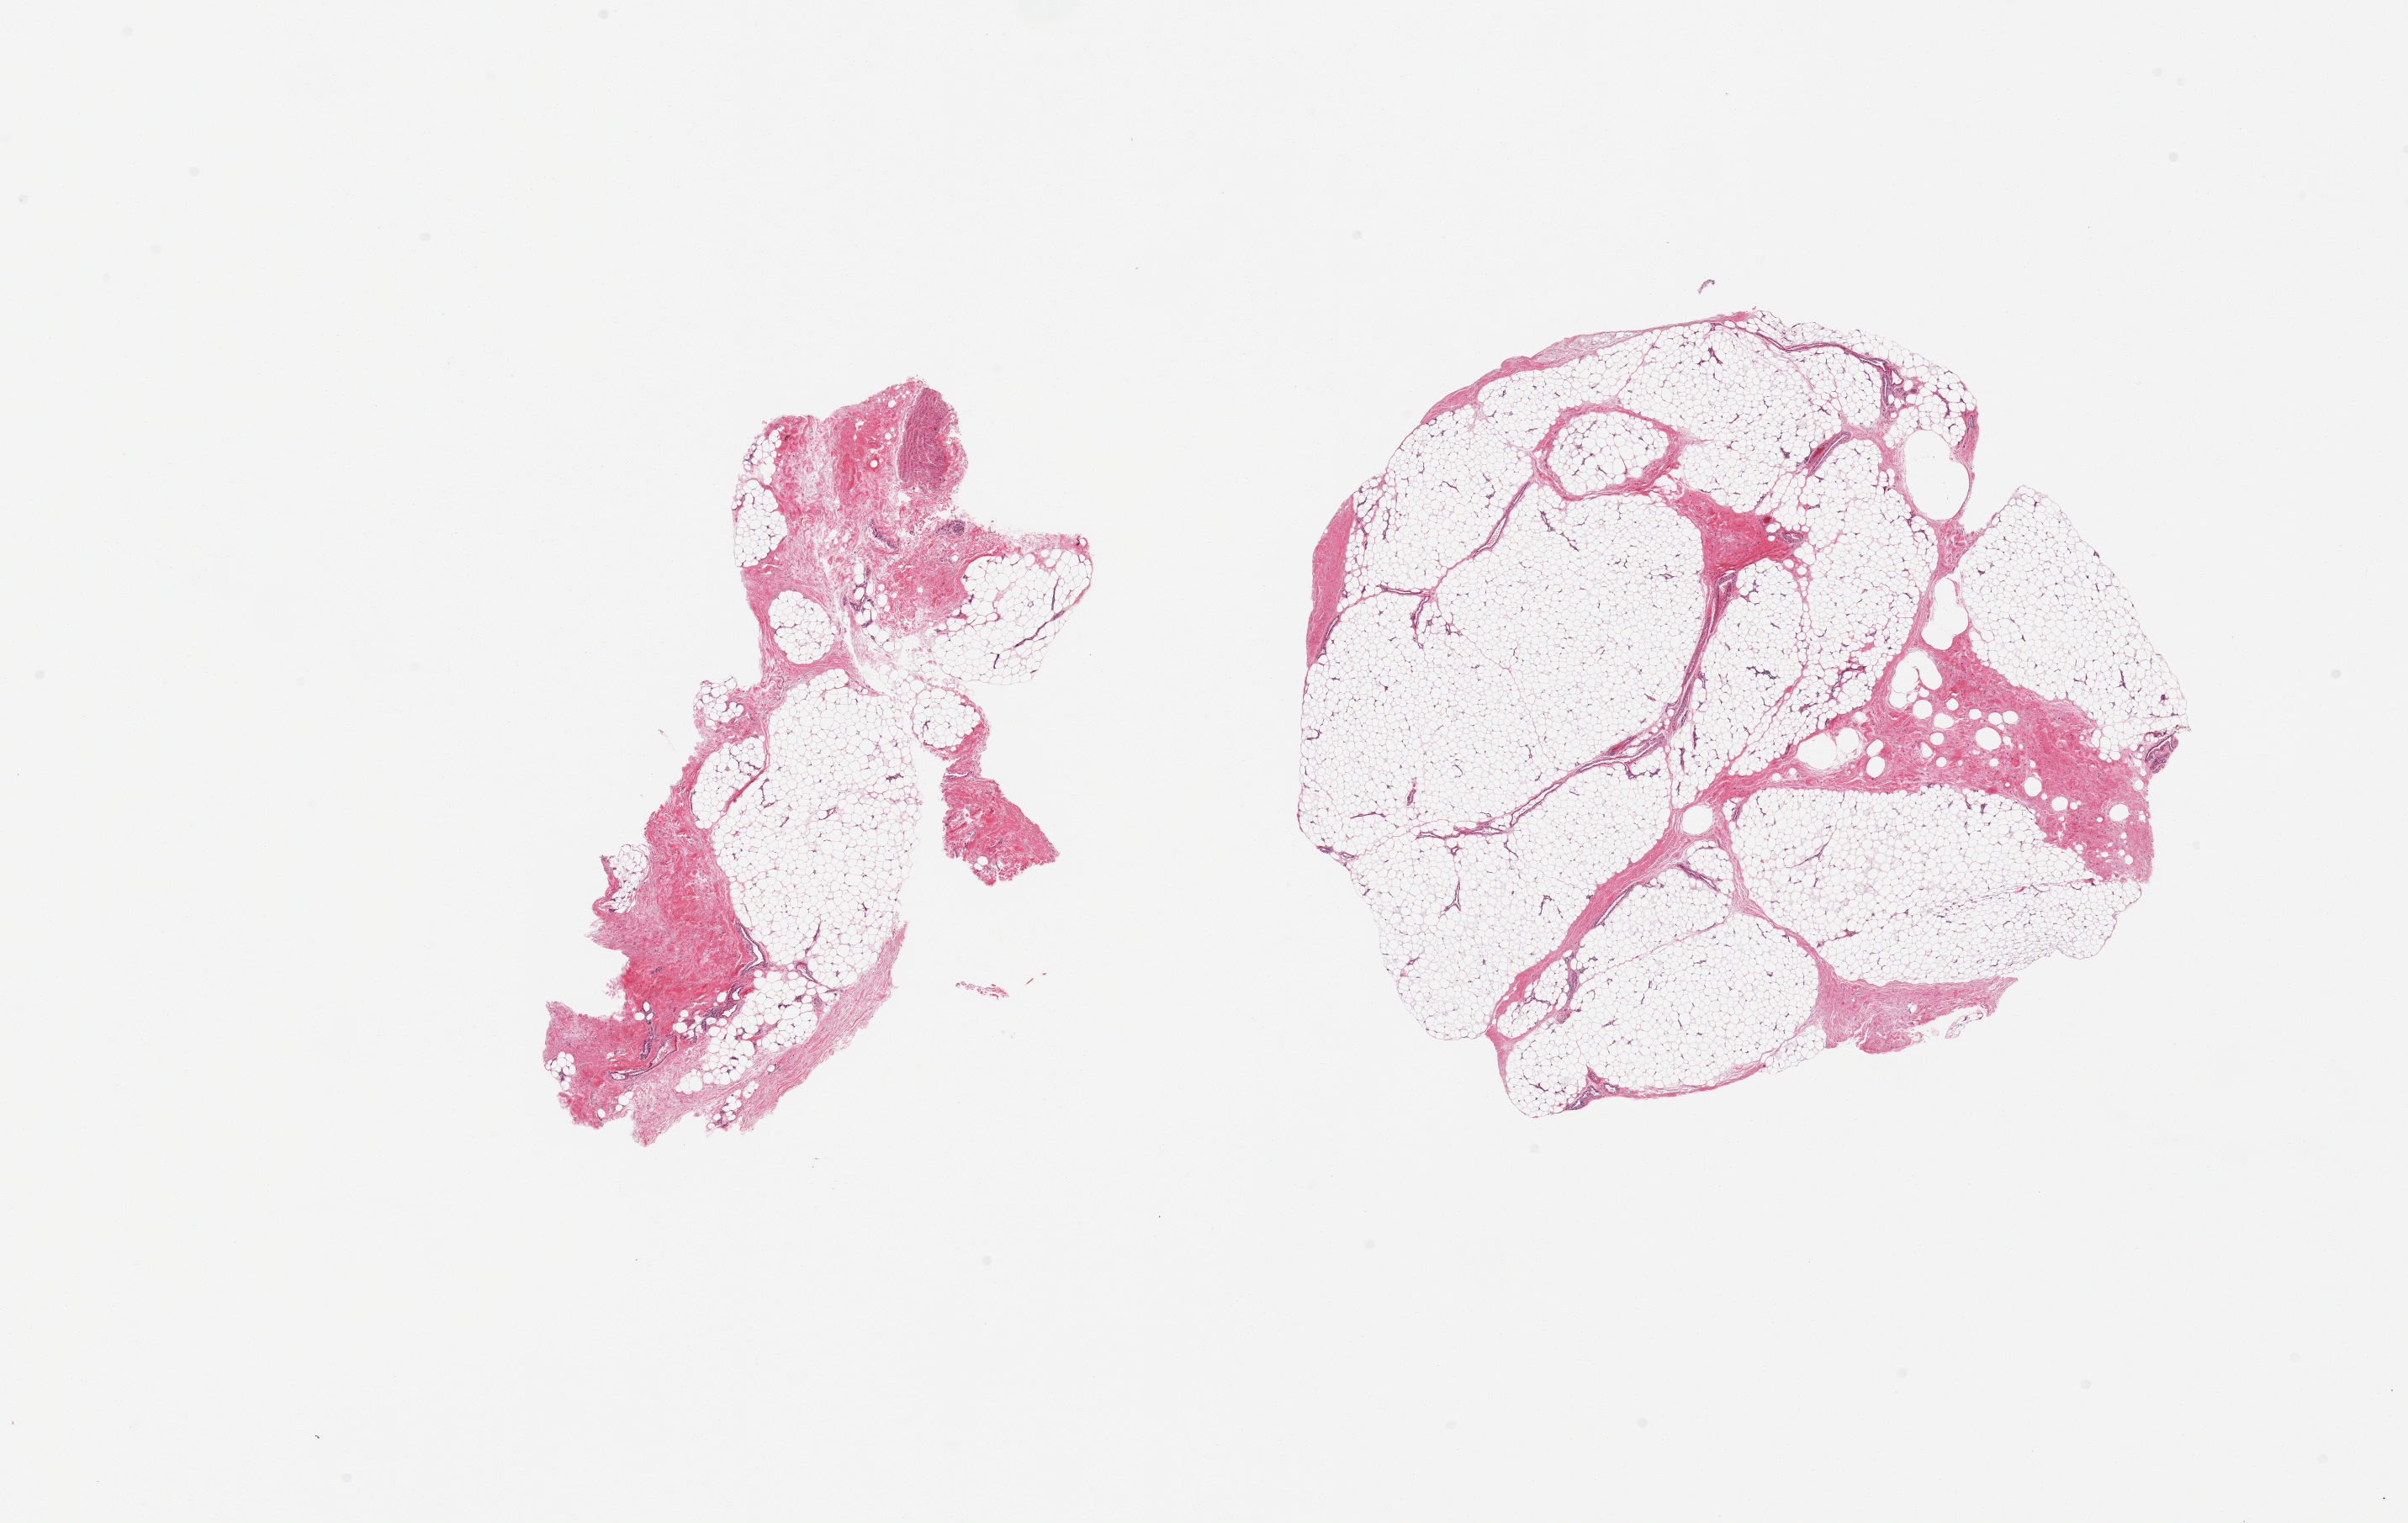
Whole-slide image, H&E stain — low-resolution overview of the scanned area, about 22.6 x 14.3 mm; PAXgene-fixed paraffin-embedded (PFPE) section; section of adipose tissue (target tissue); donor tissue sample. Donor: male.
Review note (as recorded): 2 pieces, fascia/vascular tissue is ~20%.